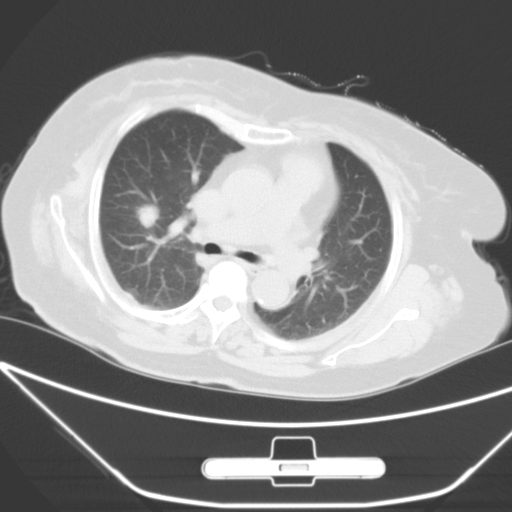
Chest CT, one axial slice. Position 33 of 49 along the scan axis. 120 kVp. Lung window (W 1500 / L -600 HU). 5 mm slice thickness. 512 × 512 image matrix, field of view 365 × 365 mm. Female patient, age 65 years. From the clinical record (not read from this slice): clinical TNM (as recorded): T1c N0 M0.
Annotated regions visible in this slice (rectangle marked by the reading radiologist):
- lung tumour (recorded histology: adenocarcinoma): box from (x=134, y=195) to (x=172, y=233) px